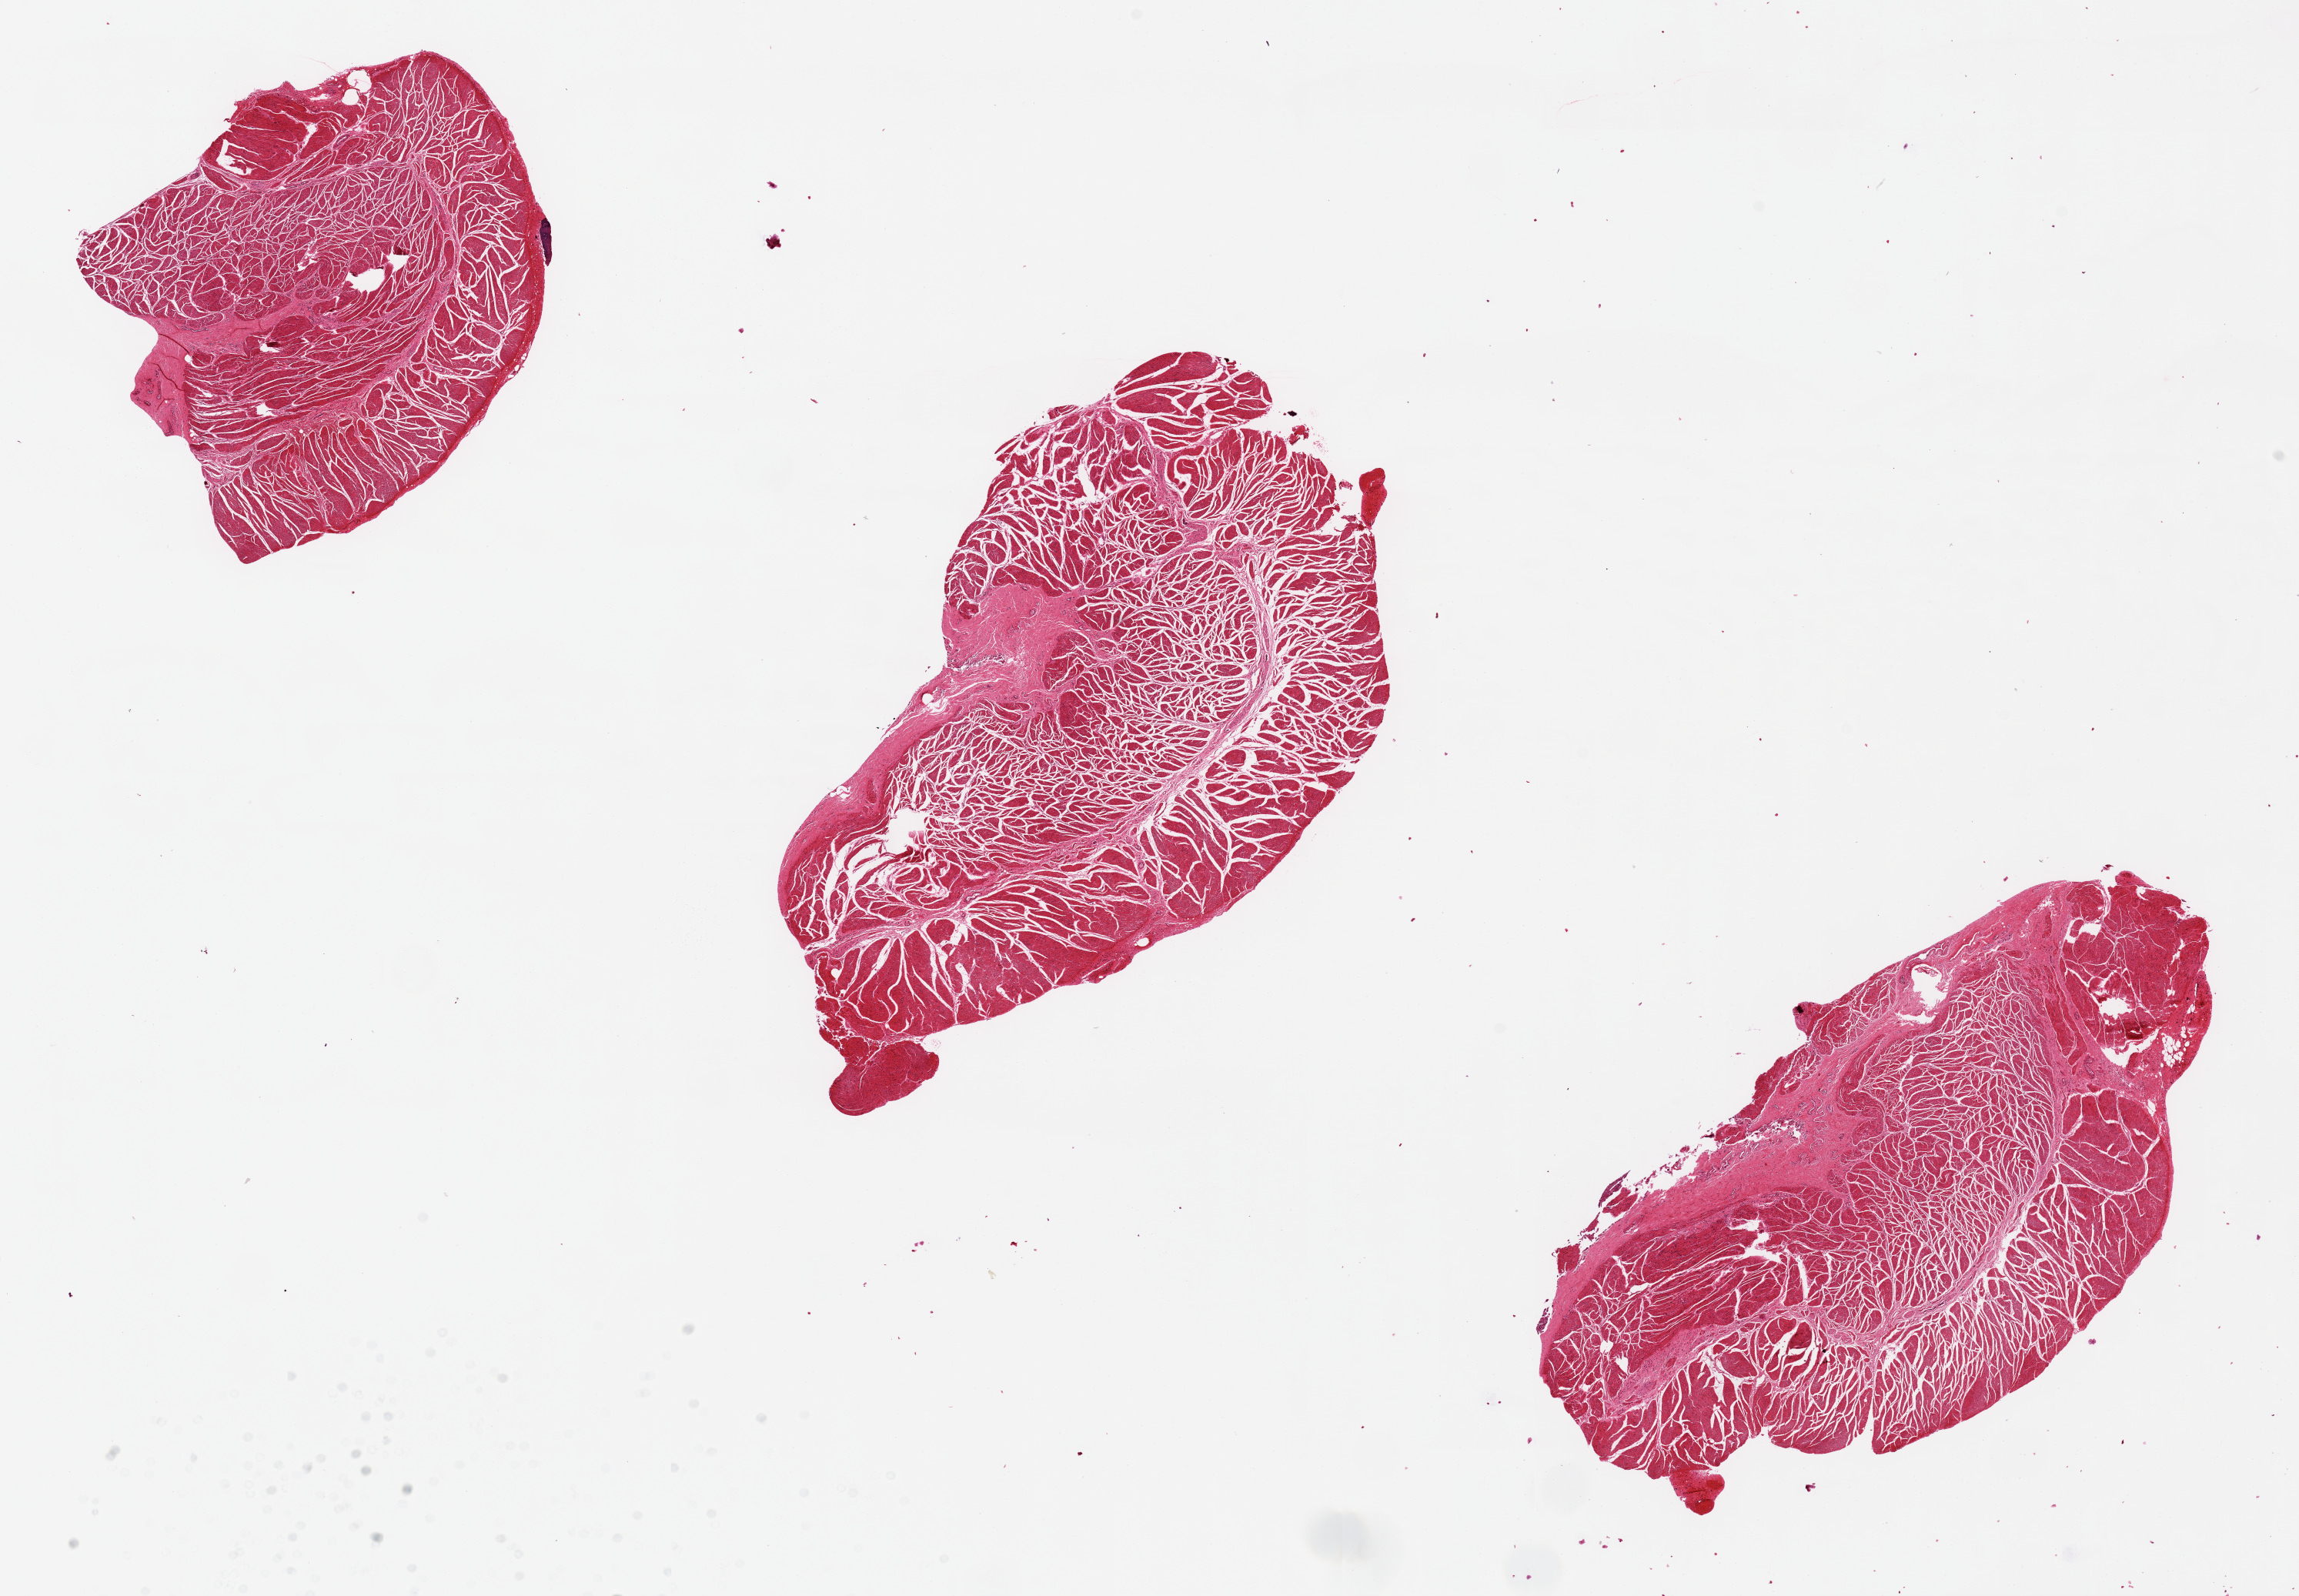
H&E whole-slide image — whole scanned area (about 23.6 x 16.4 mm) shown as a low-resolution overview, PAXgene-fixed paraffin-embedded (PFPE) section, sampled site (target tissue): esophageal muscle, donor tissue sample. Donor sex: male.
- review note (as recorded): 3 pieces; separation of muscle bundles